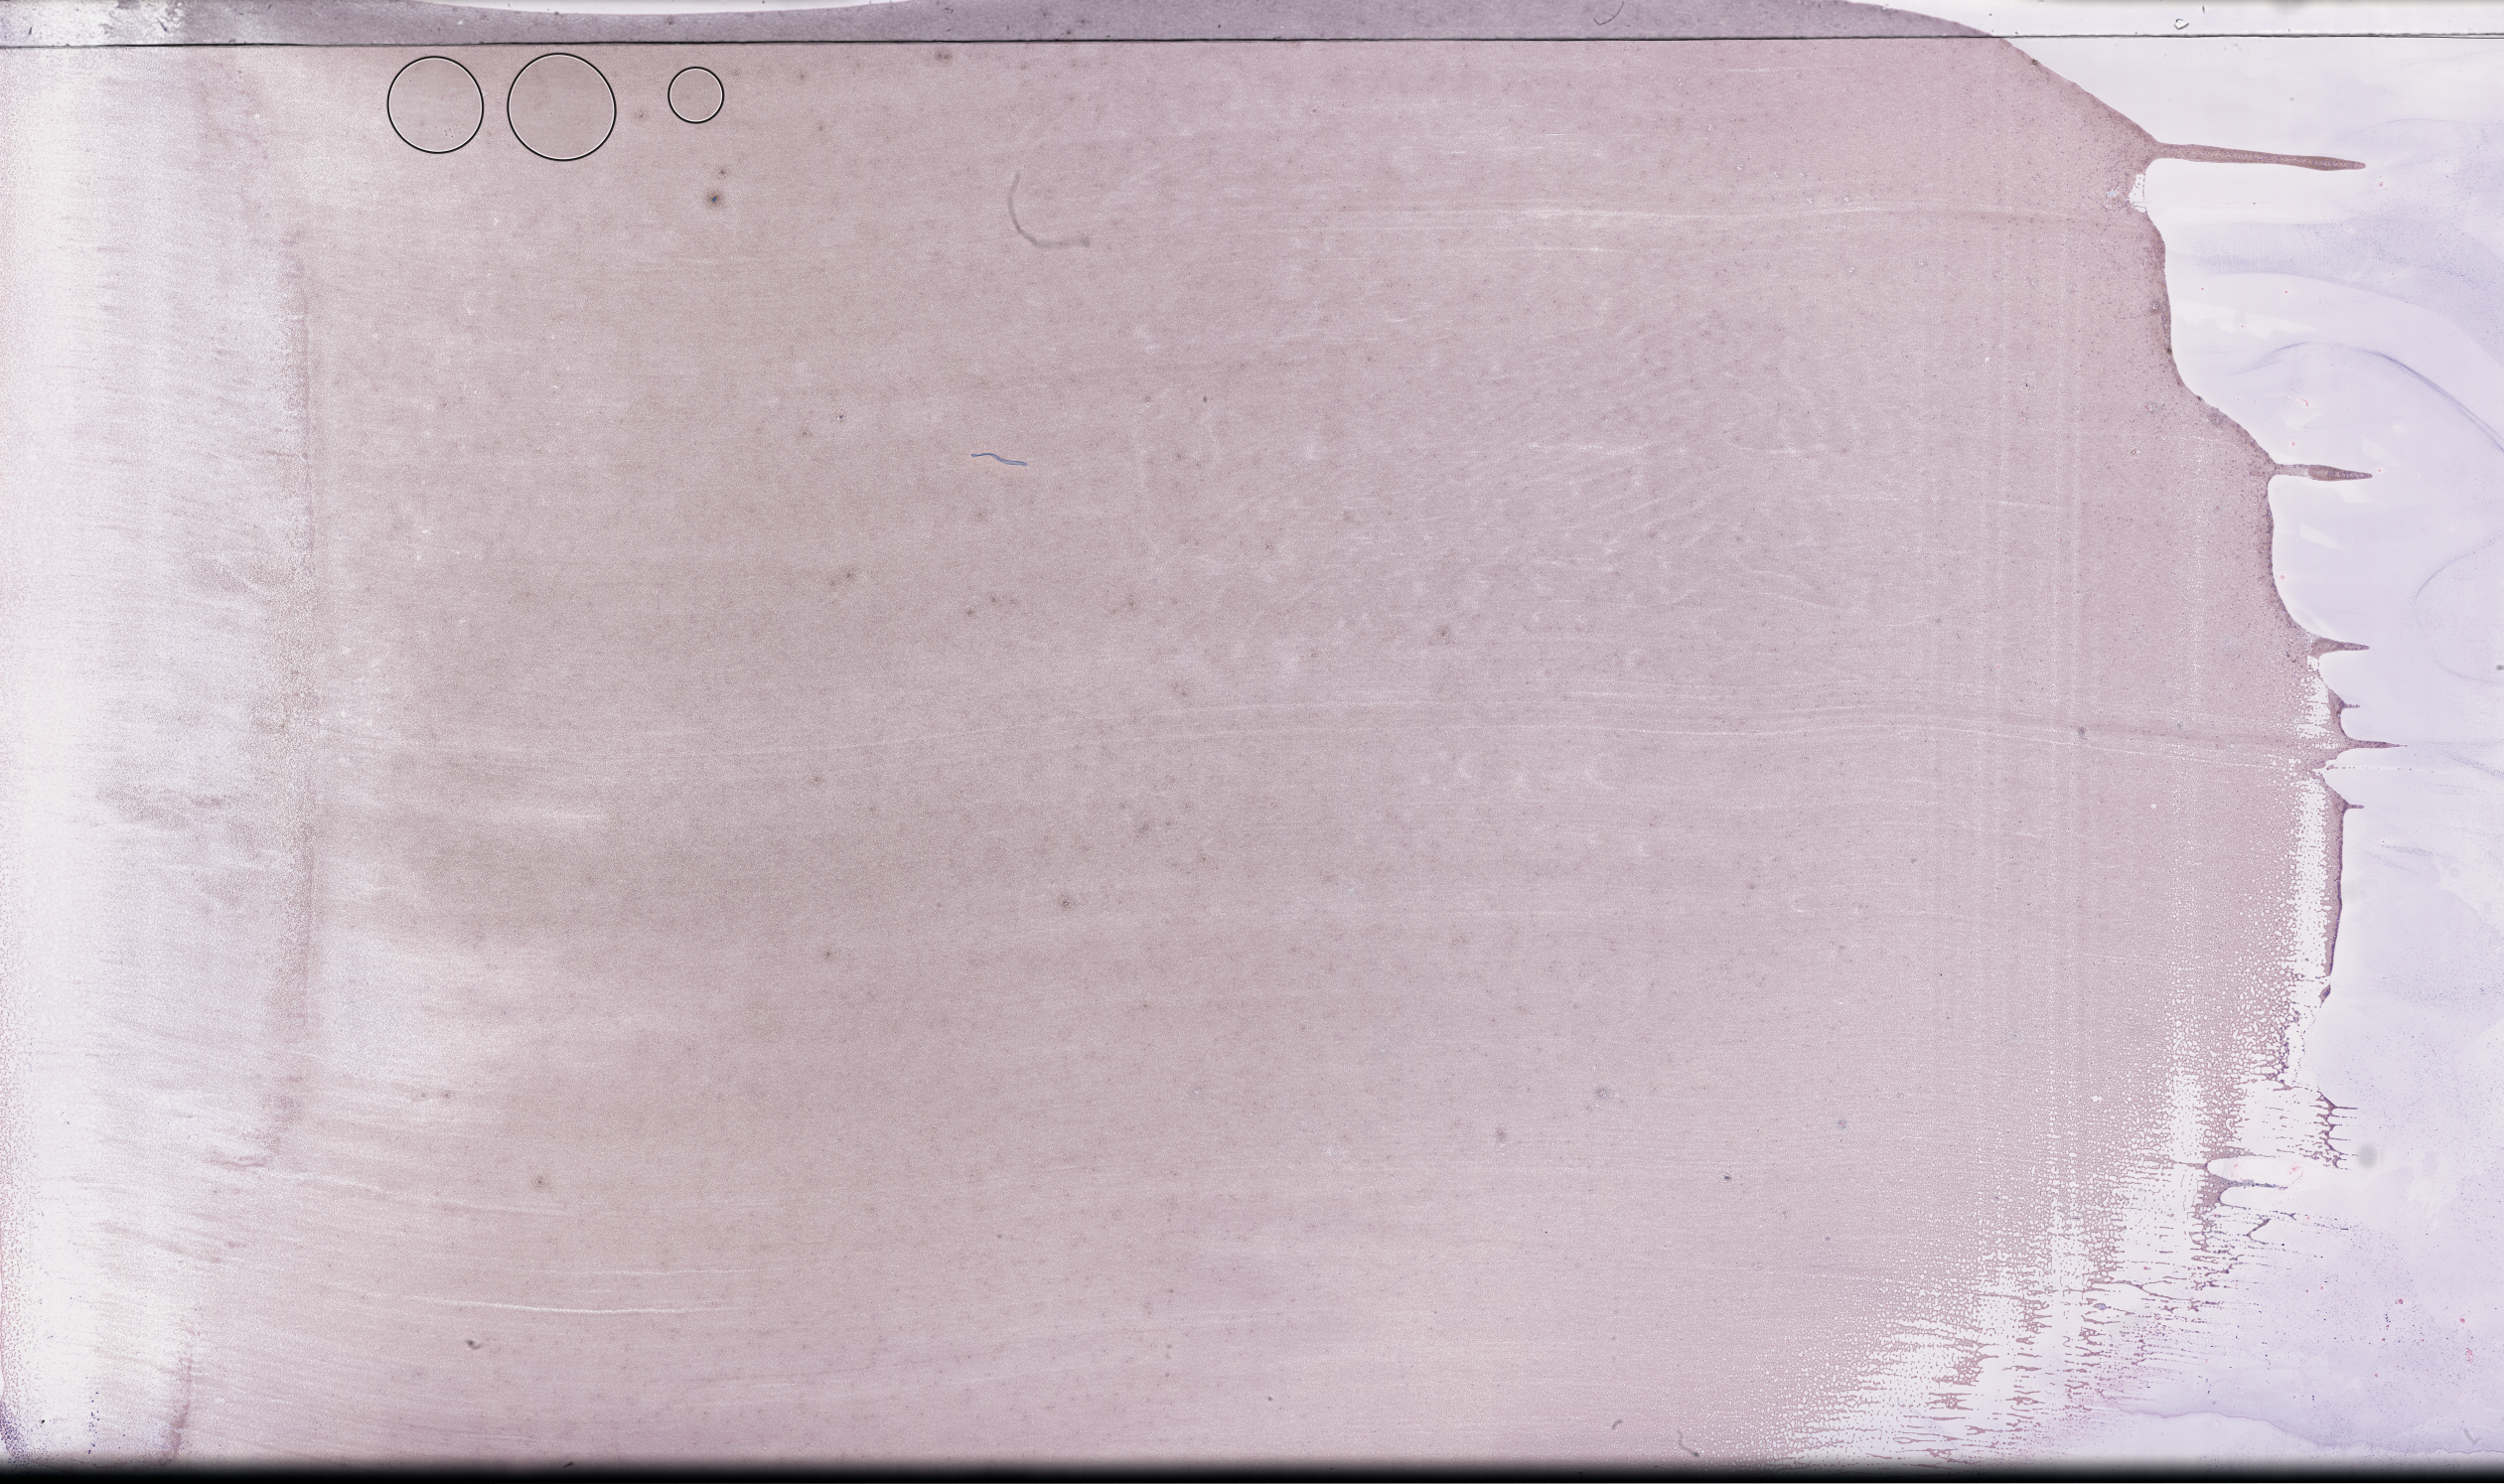
Wright-Giemsa-stained whole blood smear, whole-slide image — low-resolution overview of the scanned area, about 40.7 x 24.1 mm. Collected on treatment. Patient sex: female.
From a patient with: Plasma Cell Myeloma.